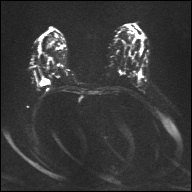
Breast MRI, one axial slice; slice 19 of 32 in the series (ordered by position); diffusion-weighted series; image 2 of 4 stored at this slice position (different b-values; order by instance number); 1.5 T; 192 × 192 image matrix. Female patient.
Outlined on this slice (outlined manually by an expert reader):
- tumour on diffusion-weighted imaging: bounding box (x1, y1, x2, y2) in pixels: (40, 78, 50, 85)